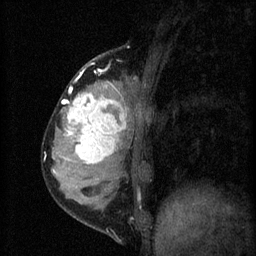
Breast MRI (dynamic contrast-enhanced), one sagittal slice; position 18 of 60 along the scan axis; 3 images stored at this slice position (order not interpretable as contrast timing); 1.5 T; TE 4.2 ms, TR 8.2 ms; 2 mm slice thickness; 256 × 256 image matrix, field of view 180 × 180 mm. Patient: female, 37 years.
Annotated regions visible in this slice (semi-automatically segmented with operator editing):
- analysis volume of interest (the breast-tissue region the enhancement analysis was run in; not a lesion): bounding box <53,78,140,181> (left, top, right, bottom; pixels)
- tumour enhancement mask (voxels above the 70 % enhancement threshold inside the analysis volume of interest): <63,86,127,165>